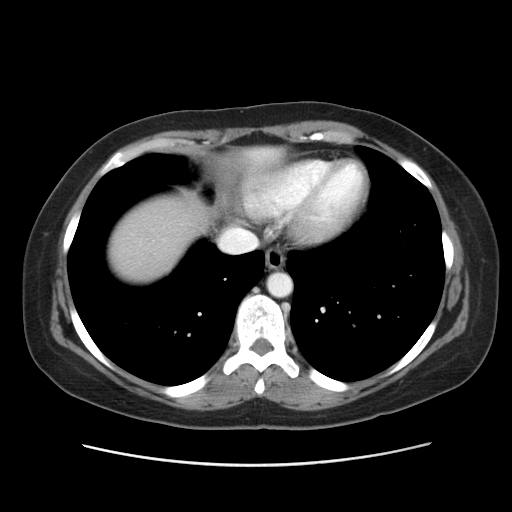
Contrast-enhanced abdominal CT, one axial slice; slice 46 of 52 in the series (ordered by position); reconstruction kernel STANDARD; 120 kVp; intravenous contrast given; soft-tissue window (W 400 / L 40 HU); 5 mm slice thickness; 512 × 512 image matrix, field of view 362 × 362 mm. Female patient, age 48 years. From the clinical record (not read from this slice): diagnosis: colorectal cancer liver metastases, imaged before liver resection; multiple liver metastases: yes; largest metastasis: 4.5 cm; disease in both lobes: yes.
Outlined on this slice (manually delineated by an expert):
- hepatic veins: bounding box (x1, y1, x2, y2) in pixels: (220, 229, 258, 248)
- liver: (110, 197, 197, 276)